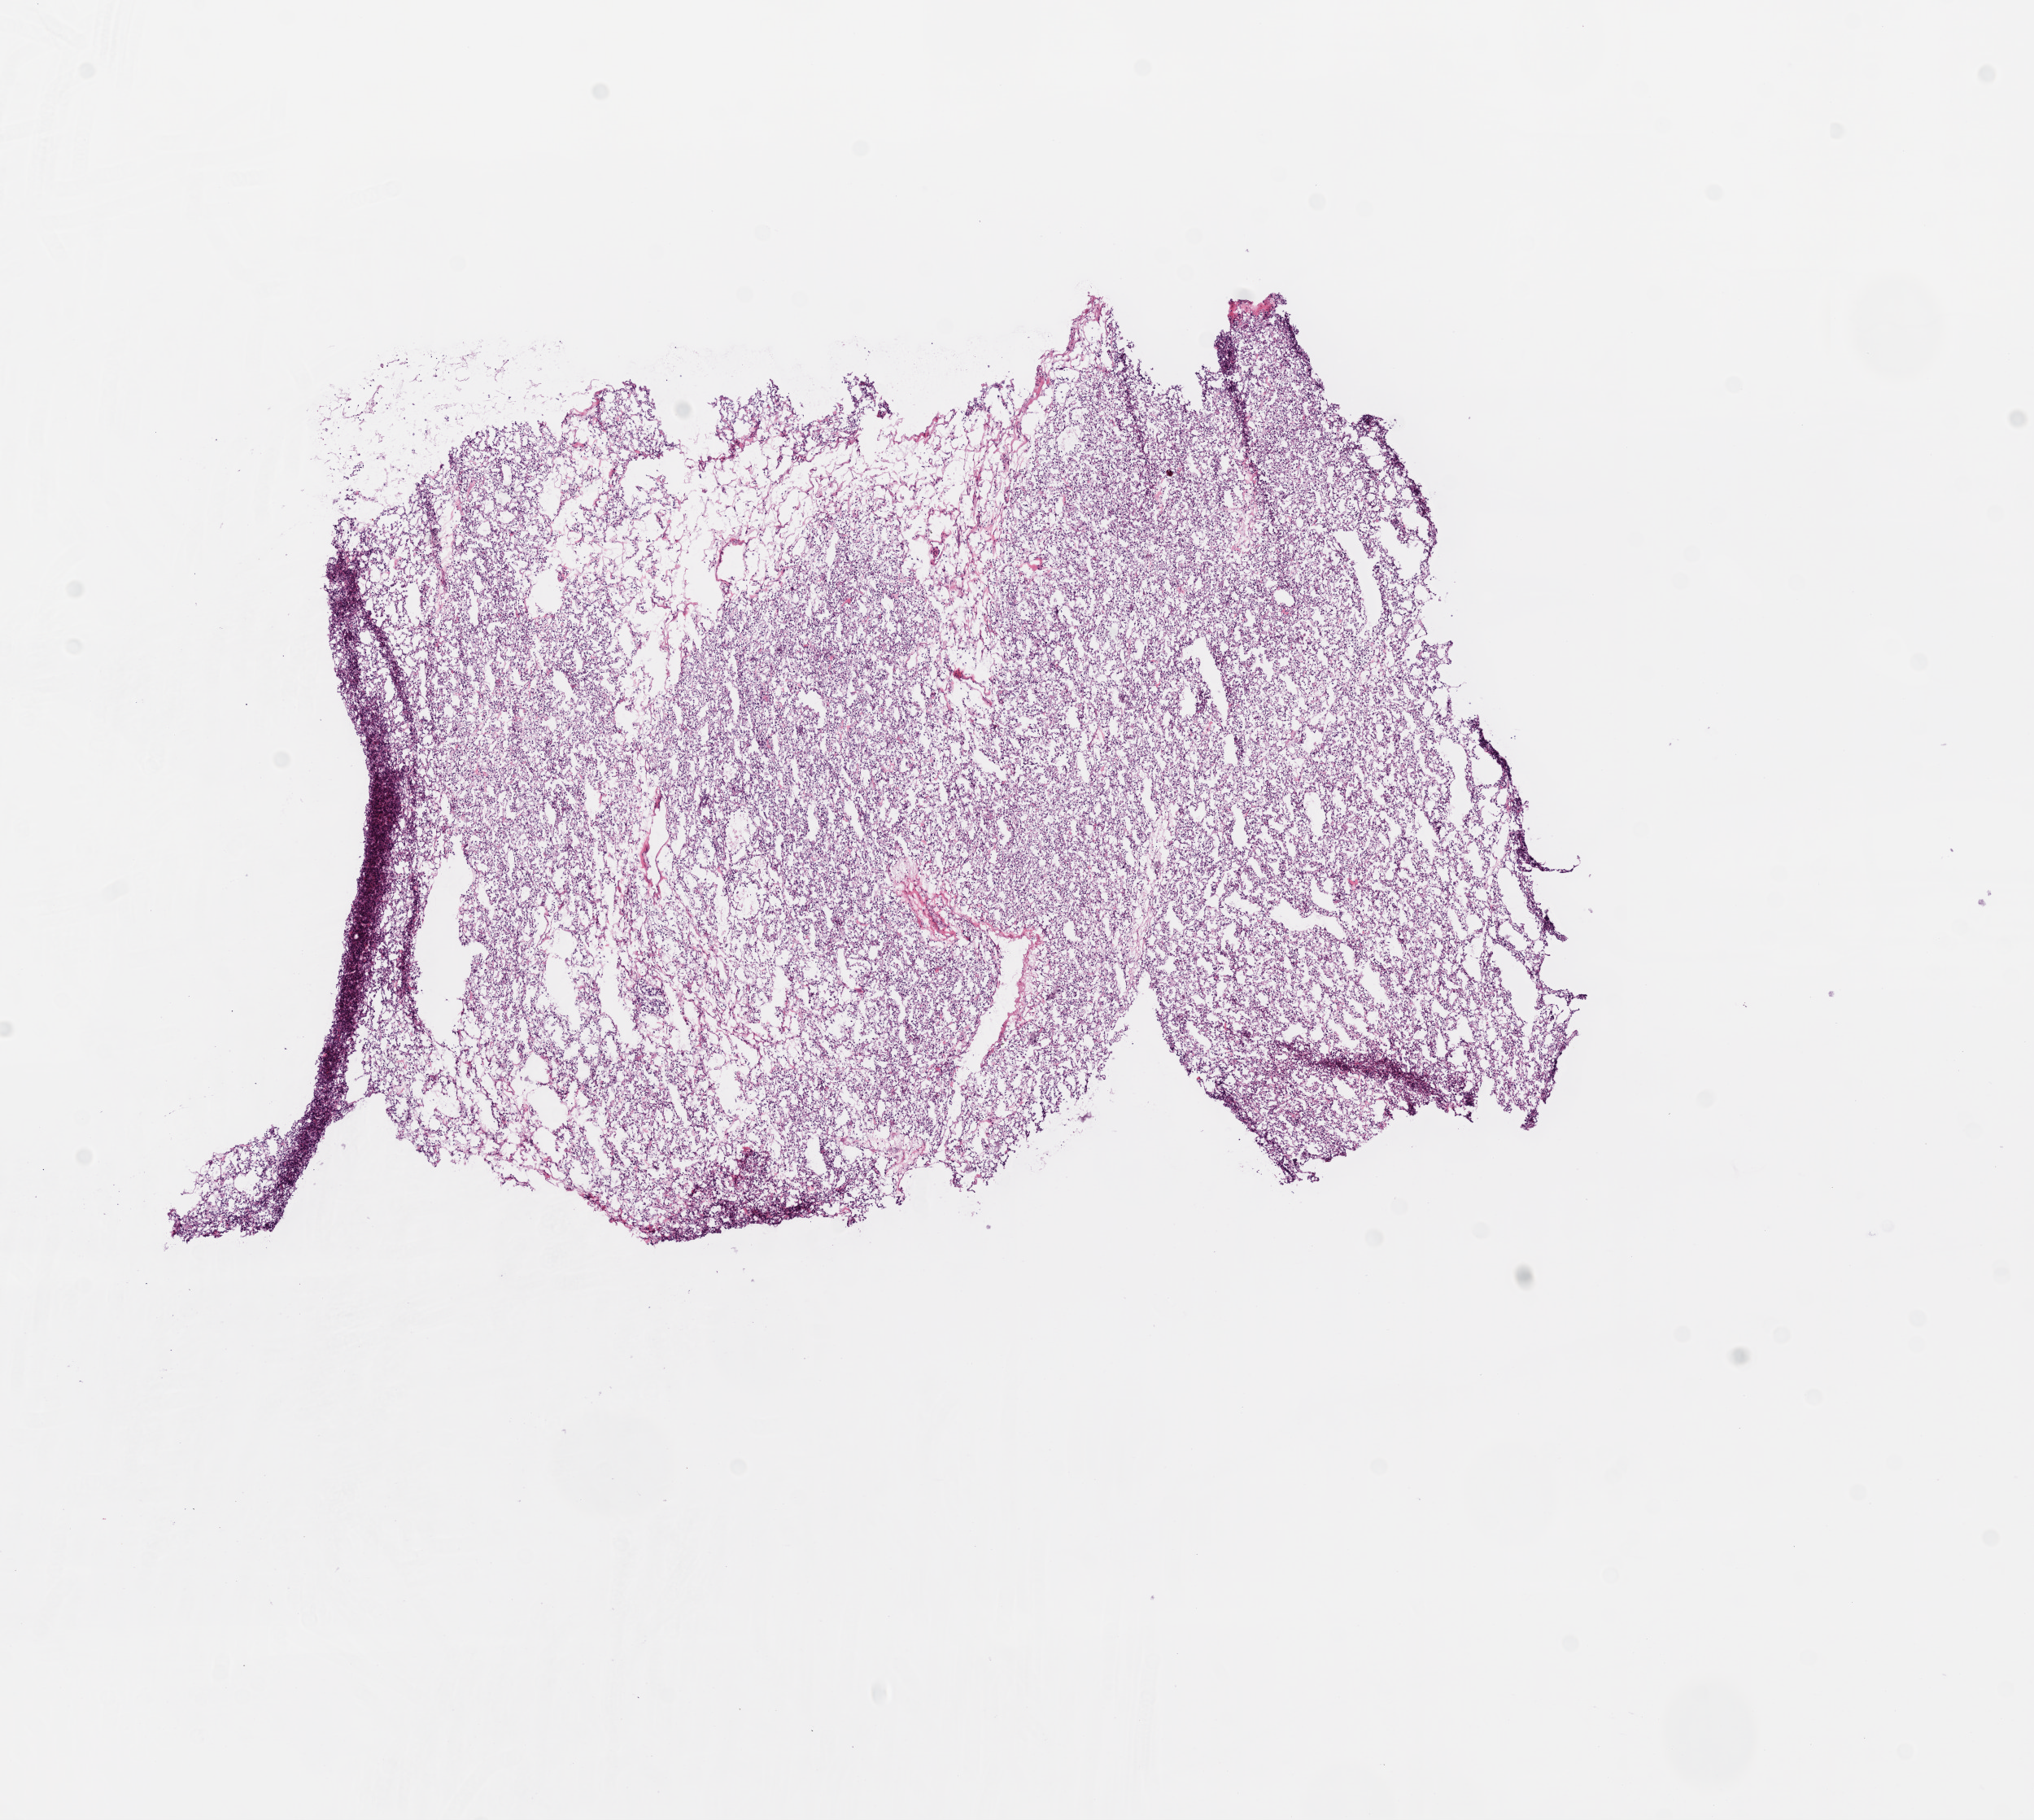
Whole-slide histology image, H&E-stained, low-resolution overview of the scanned area, about 10.0 x 9.0 mm; frozen section; primary tumour sample from the kidney. Patient: female, age at initial diagnosis 82 years. Histologic grade: G2 (moderately differentiated). Pathologist review of this section (percent, as recorded): tumour cells 90%, tumour nuclei 80%, normal cells 0%, stromal cells 10%, necrosis 0%.
* AJCC pathologic stage: I
* diagnosis: Clear cell adenocarcinoma, NOS